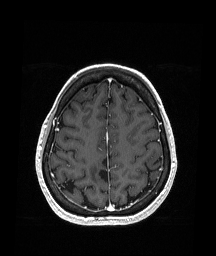
Brain MRI from a brain-tumour surgery series, one axial slice. Position 59 of 151 along the scan axis. T1-weighted post-contrast. 216 × 256 image matrix, field of view 211 × 250 mm. Case-level facts recorded for this patient, not image findings: histopathology: Oligodendroglioma; WHO grade: 2; IDH mutation: yes.
Annotated regions visible in this slice (outlined manually by an expert reader):
- previous resection cavity: bounding box (x1, y1, x2, y2) in pixels: (94, 155, 109, 180)